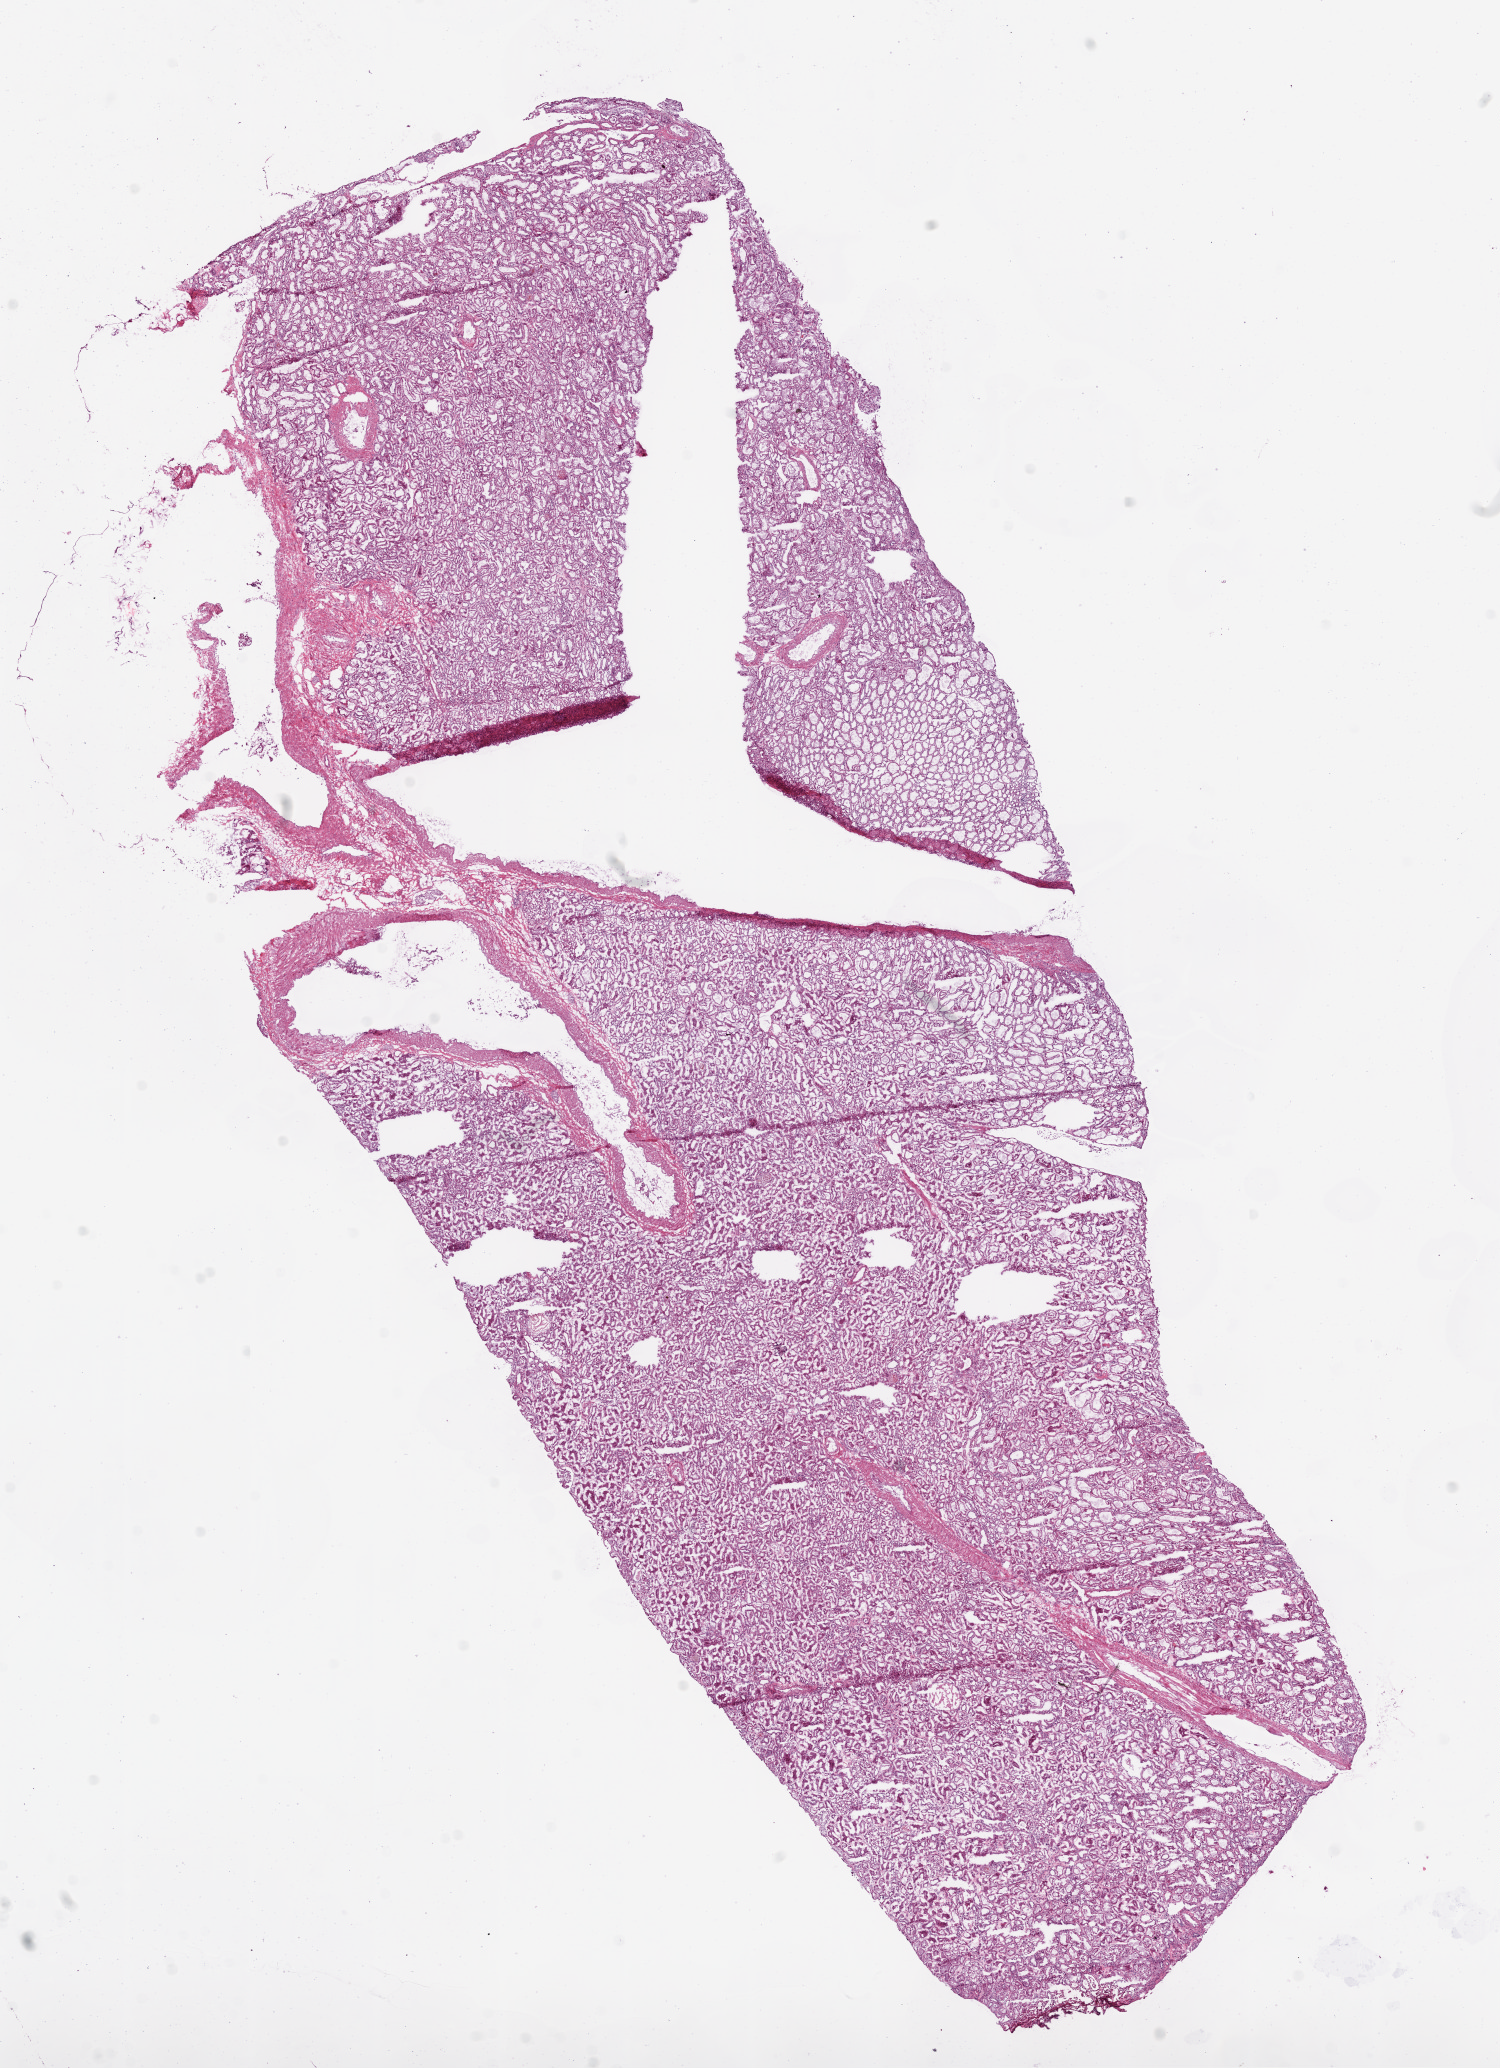
H&E-stained whole-slide image, low-resolution overview of the scanned area, about 12.0 x 16.6 mm (from a 20x scan), frozen section, solid tissue normal (non-tumour tissue) sample from the kidney. Patient: male, age at initial diagnosis 47 years.
• this section: solid tissue normal sample (biorepository sample class)
• patient diagnosis: Clear cell adenocarcinoma, NOS